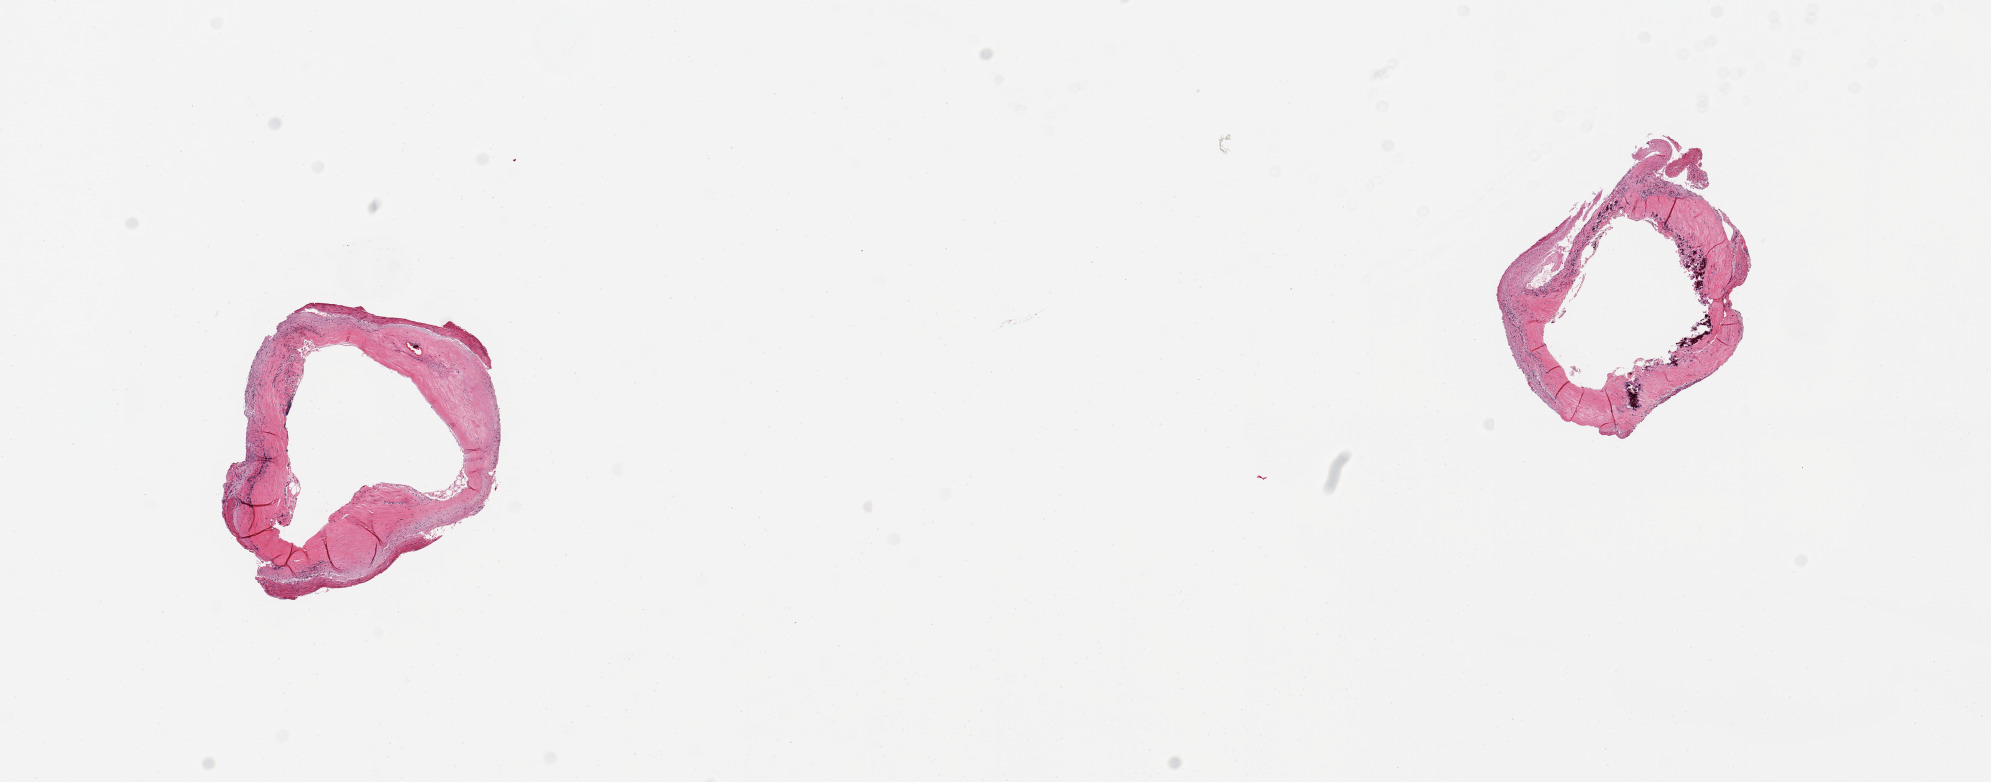
H&E whole-slide image, brightfield — shown as a low-resolution overview of the whole scanned area (about 15.8 x 6.2 mm). PAXgene-fixed paraffin-embedded (PFPE) section. Target tissue: coronary artery. Donor tissue sample.
Pathologist's review note for this sample: 2 pieces; 2x2 & 2x2mm; calcified atherosclerosis with ~60% occlusion.